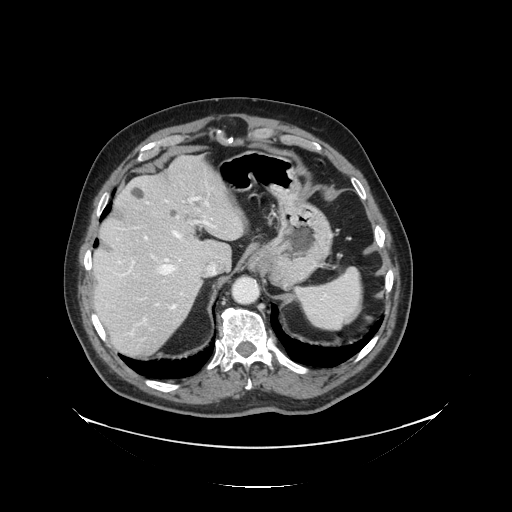
Contrast-enhanced abdominal CT, one axial slice; slice 103 of 138 in the series (ordered by position); reconstruction kernel STANDARD; 120 kVp; soft-tissue window (W 400 / L 40 HU); 2.5 mm slice thickness; 512 × 512 image matrix, field of view 497 × 497 mm. Male patient, age 77 years. Case-level facts recorded for this patient, not image findings: diagnosis: colorectal cancer liver metastases, imaged before liver resection; multiple liver metastases: no; largest metastasis: 1.5 cm.
Annotated regions visible in this slice (outlined manually by an expert reader):
- hepatic veins: bounding box <157,201,213,310> (left, top, right, bottom; pixels)
- liver: <93,157,245,358>
- planned liver remnant (the part of the liver to remain after resection): <92,157,245,289>
- portal vein (with intrahepatic branches): <129,197,217,324>
- liver metastasis: <169,208,180,219>
- liver metastasis: <131,187,144,199>